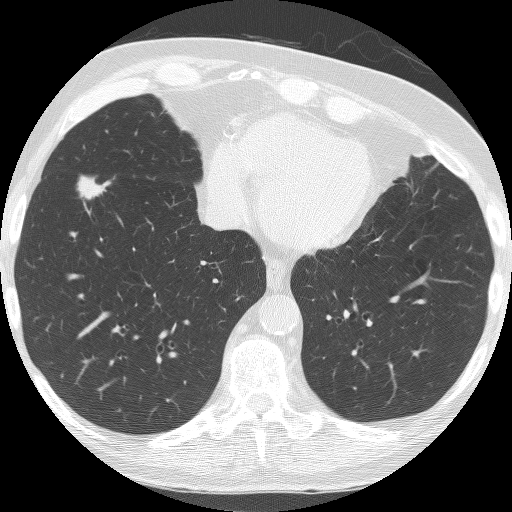
Axial slice from a low-dose chest CT screening exam. Baseline screening round. Lung window (W 1500 / L -600 HU). 120 kVp. Slice 116 of 182 in the series. Male, age 74 years at enrolment. Former smoker at enrolment.
Expert-annotated lung lesion, bounding box (x1, y1, x2, y2) in pixels: (70, 167, 119, 206). The screening reader recorded 4 non-calcified nodules or masses ≥4 mm on this exam (right lower lobe, right lower lobe, right lower lobe, right lower lobe); which of them this box marks is not recorded. Official screen result: positive, change unspecified: nodule(s) >= 4 mm or enlarging nodule(s), mass(es), or other non-specific abnormalities suspicious for lung cancer.